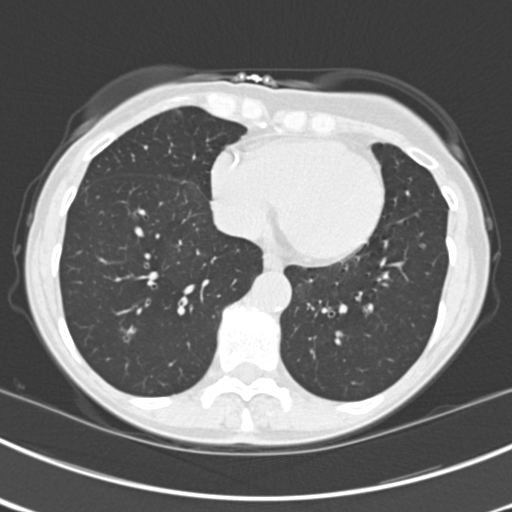
Low-dose screening chest CT, axial slice. Third annual screen. Lung window (W 1500 / L -600 HU). 512 × 512 image matrix, field of view 302 × 302 mm. Female participant, aged 63 years at enrolment. Current smoker at enrolment.
Expert-annotated lung lesion, bounding box <104,312,149,359> (left, top, right, bottom; pixels). The screening reader recorded 9 non-calcified nodules or masses ≥4 mm on this exam (left upper lobe, right upper lobe, left upper lobe, left lower lobe, right middle lobe, left lower lobe, left lower lobe, right lower lobe, right lower lobe); which of them this box marks is not recorded. Participant outcome: lung cancer diagnosed 15 days after this screen — bronchiolo-alveolar adenocarcinoma, NOS, right upper lobe, right middle lobe, right lower lobe, left upper lobe, left lower lobe, moderately differentiated (G2), stage IV (AJCC 6th edition).